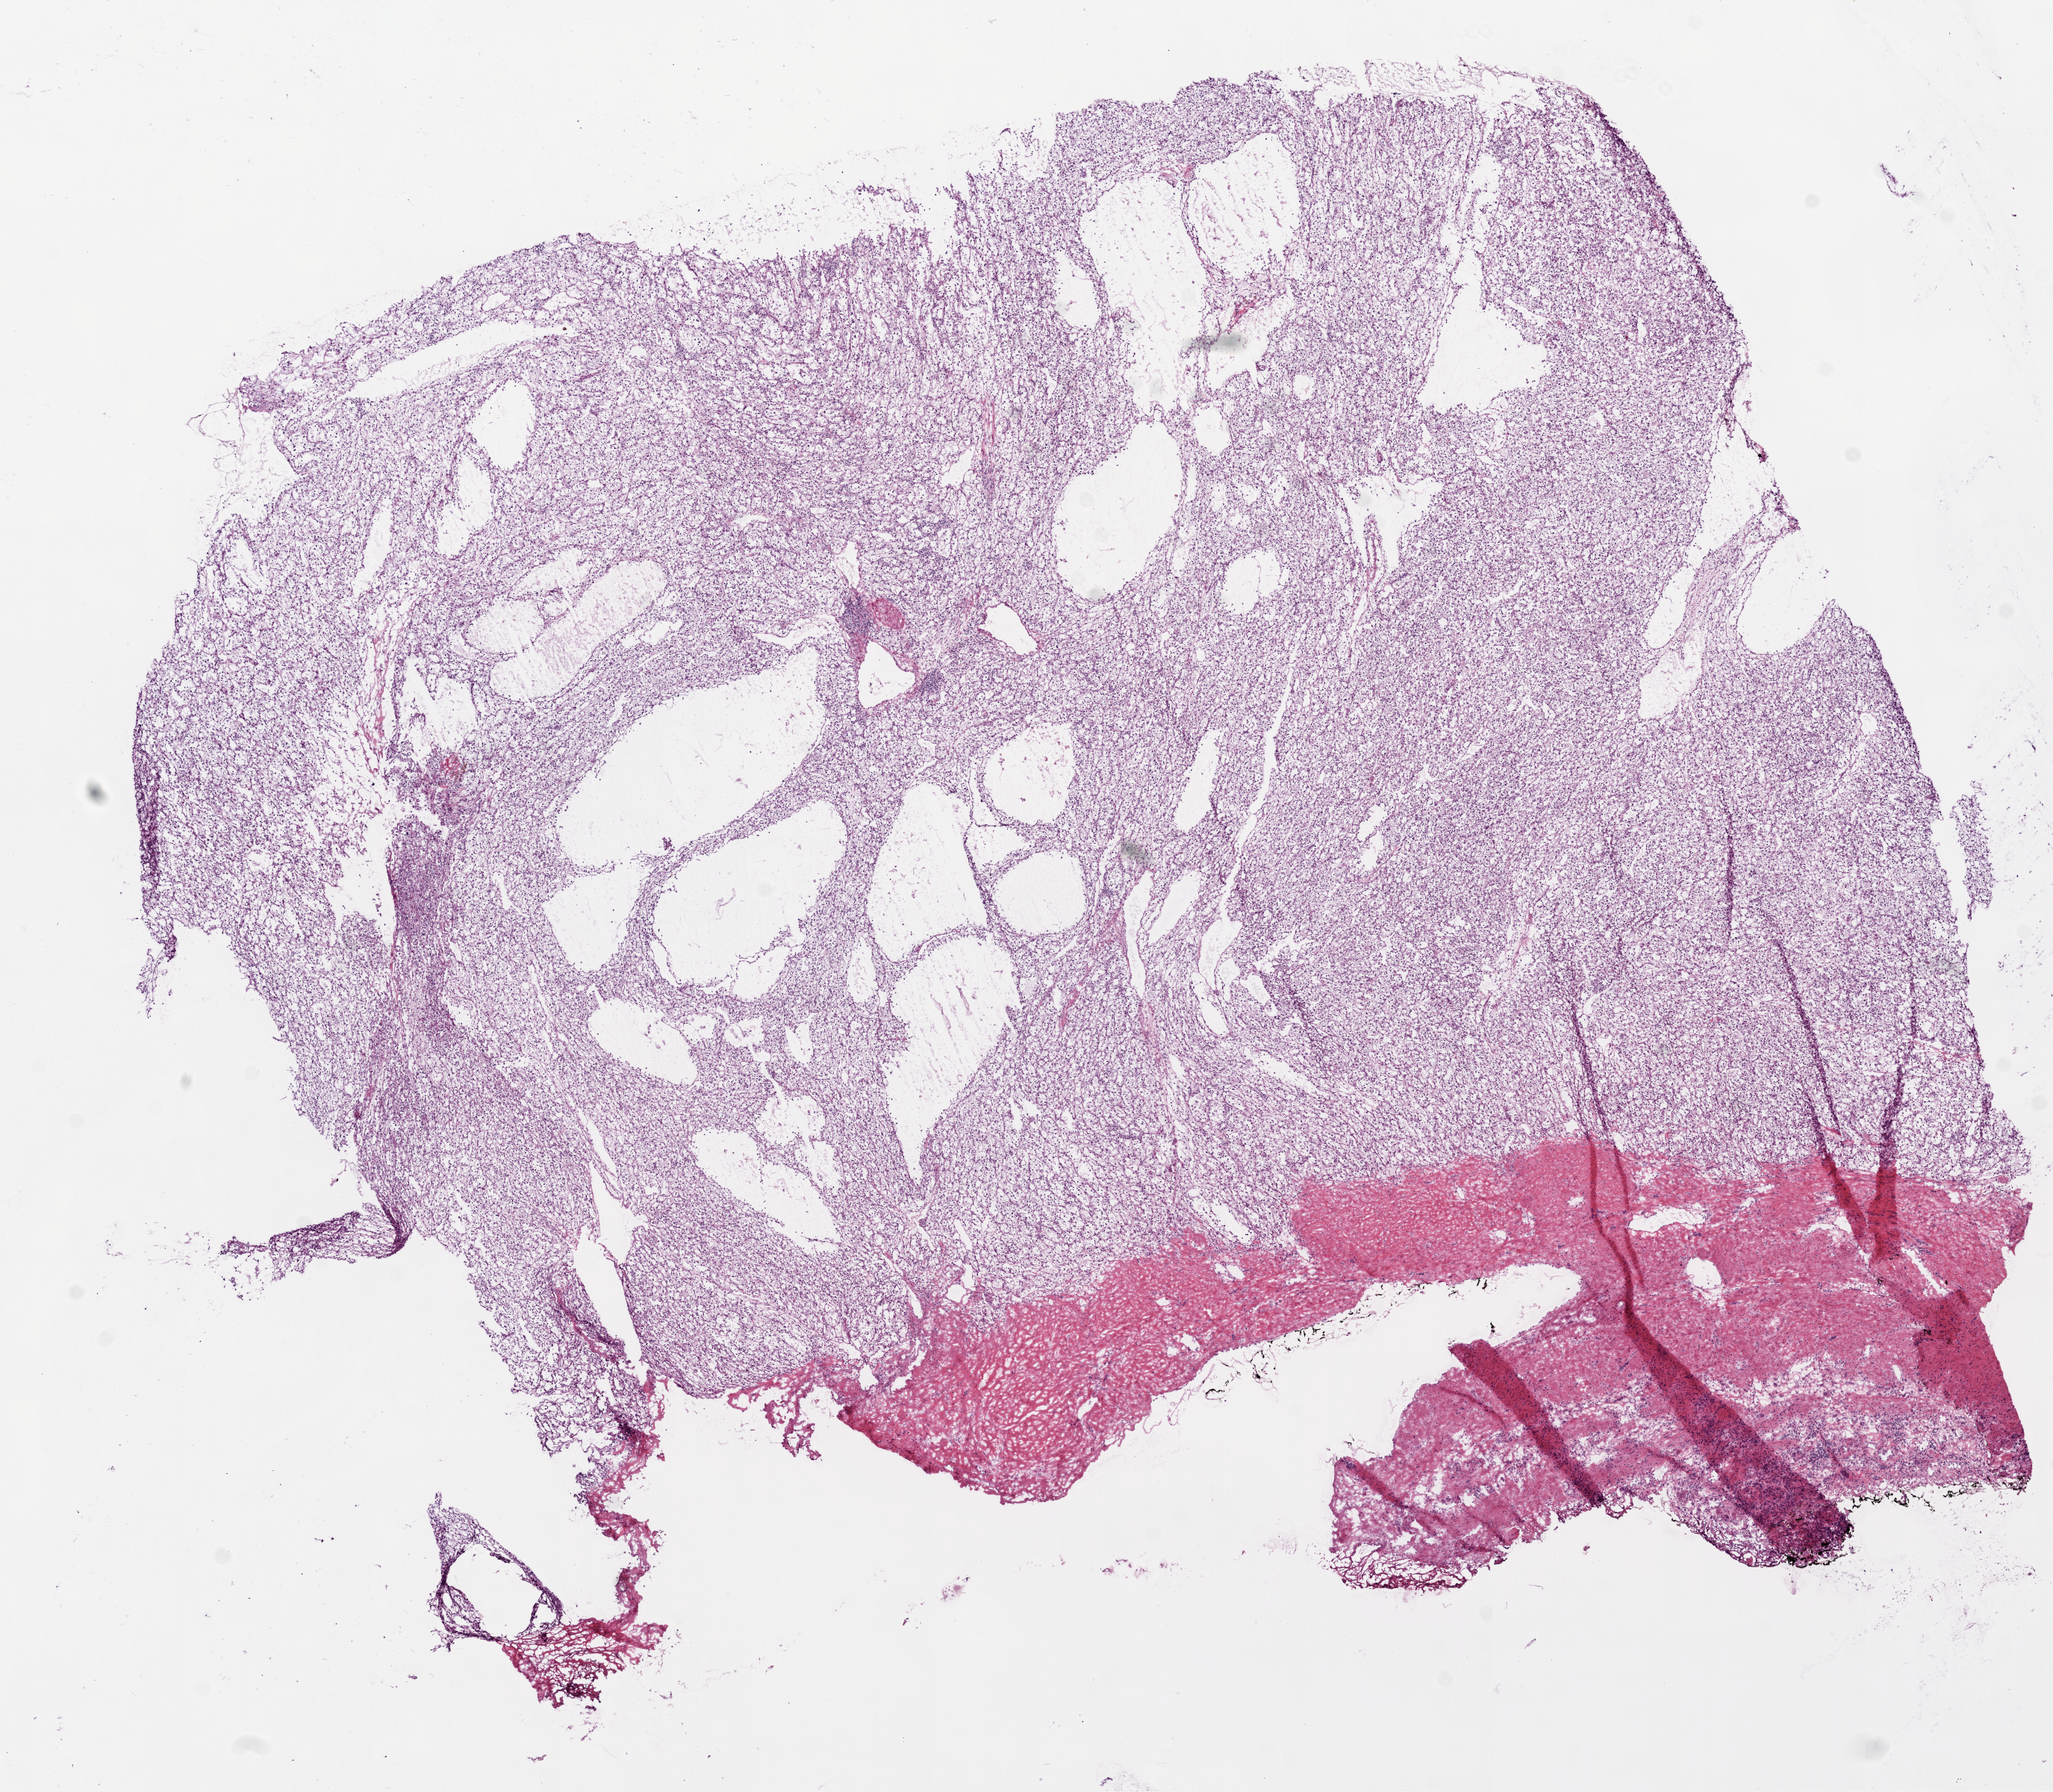
Digitized H&E-stained tissue section (whole slide) — a low-resolution overview of the entire scanned area, about 11.0 x 9.6 mm (slide scanned at 20x), frozen section, sample: primary tumour, kidney. Female, age 48 years at initial diagnosis. Histologic grade: G2 (moderately differentiated). Slide review estimates, as recorded: tumour cells 90%, tumour nuclei 80%, normal cells 0%, stromal cells 10%, necrosis 0%.
AJCC pathologic stage: I. Pathologic diagnosis: Clear cell adenocarcinoma, NOS.